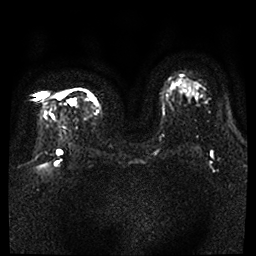
Breast MRI, one axial slice; diffusion-weighted series; image 2 of 4 stored at this slice position (different b-values; order by instance number); 1.5 T; 4 mm slice thickness; 256 × 256 image matrix, field of view 360 × 360 mm. Female patient.
Annotated regions visible in this slice (expert manual segmentation):
- tumour on diffusion-weighted imaging: box from (x=57, y=93) to (x=75, y=104) px